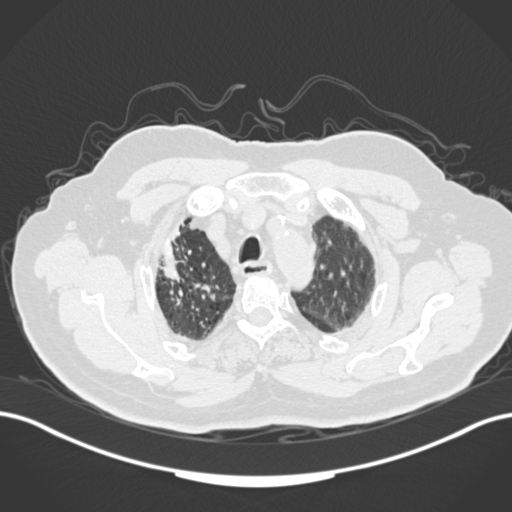
Chest CT, one axial slice. Position 140 of 205 along the scan axis. Lung window (W 1500 / L -600 HU). 1 mm slice thickness. 512 × 512 image matrix. Patient: male, 72 years. Case-level facts recorded for this patient, not image findings: clinical TNM (as recorded): T1a N0 M0.
Structures marked on this image (rectangle marked by the reading radiologist):
- lung tumour (recorded histology: squamous cell carcinoma): bounding box (x1, y1, x2, y2) in pixels: (156, 228, 187, 281)